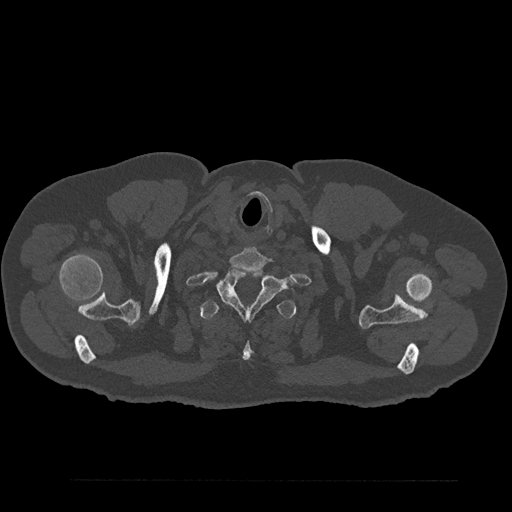
CT including the spine, one axial slice; slice 748 of 797 in the series (ordered by position); reconstruction kernel Br40s/3; bone window (W 1800 / L 400 HU); 0.5 mm slice thickness; 512 × 512 image matrix, field of view 430 × 430 mm. Male patient, age 61 years. From the clinical record (not read from this slice): primary cancer: prostate.
Outlined on this slice (semi-automatic segmentation, software-assisted and operator-edited):
- T1 vertebra: box from (x=218, y=268) to (x=293, y=320) px
- T2 vertebra: (x=200, y=299)–(x=296, y=361)